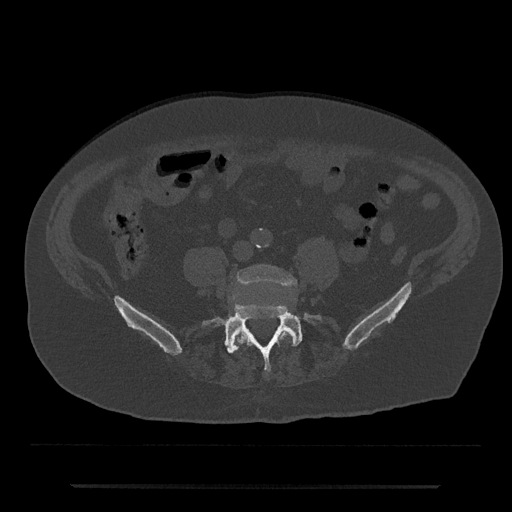
CT including the spine, one axial slice. Reconstruction kernel Br40s/3. 120 kVp. Bone window (W 1800 / L 400 HU). 0.5 mm slice thickness. 512 × 512 image matrix, field of view 434 × 434 mm. Male patient, age 80 years. Case-level facts recorded for this patient, not image findings: primary cancer: prostate; vertebrae with lytic lesions (as recorded): L1, T11.
Annotated regions visible in this slice (semi-automatic segmentation, software-assisted and operator-edited):
- L4 vertebra: bounding box <234,265,297,346> (left, top, right, bottom; pixels)
- L5 vertebra: <202,303,322,372>